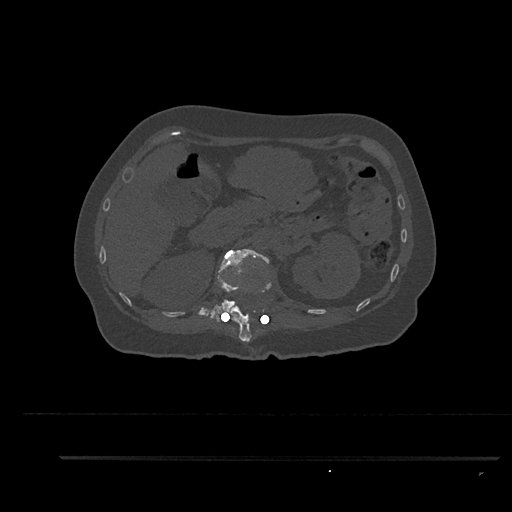
CT including the spine, one axial slice; slice 236 of 797 in the series (ordered by position); 120 kVp; bone window (W 1800 / L 400 HU); 512 × 512 image matrix, field of view 408 × 408 mm. Female patient, age 44 years. Case-level facts recorded for this patient, not image findings: primary cancer: renal.
Annotated regions visible in this slice (semi-automatically segmented with operator editing):
- L1 vertebra: box from (x=210, y=249) to (x=270, y=319) px
- T12 vertebra: (x=215, y=257)–(x=272, y=343)